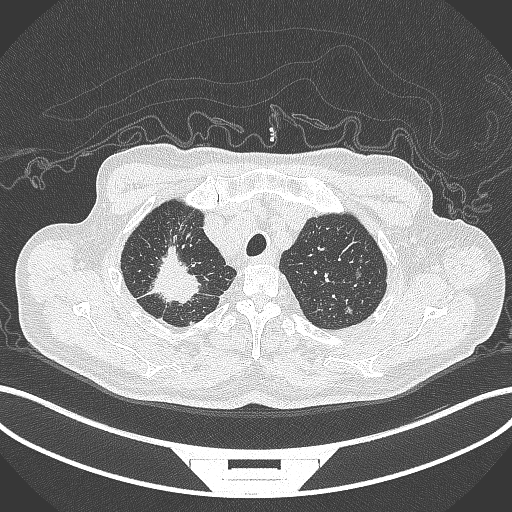
Chest CT, one axial slice; slice 329 of 407 in the series (ordered by position); reconstruction kernel B70f; lung window (W 1500 / L -600 HU); 1 mm slice thickness; 512 × 512 image matrix, field of view 400 × 400 mm. Patient: male, 69 years. From the clinical record (not read from this slice): clinical TNM (as recorded): T1c N1 M1.
Outlined on this slice (bounding box drawn by a radiologist):
- lung tumour (recorded histology: adenocarcinoma): bounding box <142,242,211,307> (left, top, right, bottom; pixels)